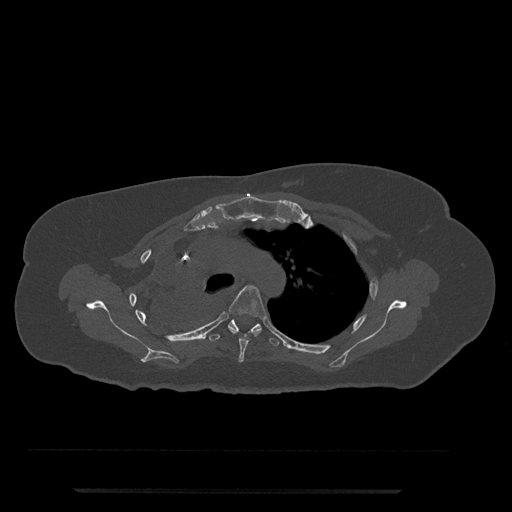
CT including the spine, one axial slice; position 571 of 797 along the scan axis; 120 kVp; bone window (W 1800 / L 400 HU); 0.5 mm slice thickness; 512 × 512 image matrix, field of view 440 × 440 mm. Female patient, age 51 years. From the clinical record (not read from this slice): primary cancer: neuro.
Annotated regions visible in this slice (semi-automatically segmented with operator editing):
- T4 vertebra: bounding box <229,285,267,362> (left, top, right, bottom; pixels)
- T5 vertebra: <209,319,279,346>